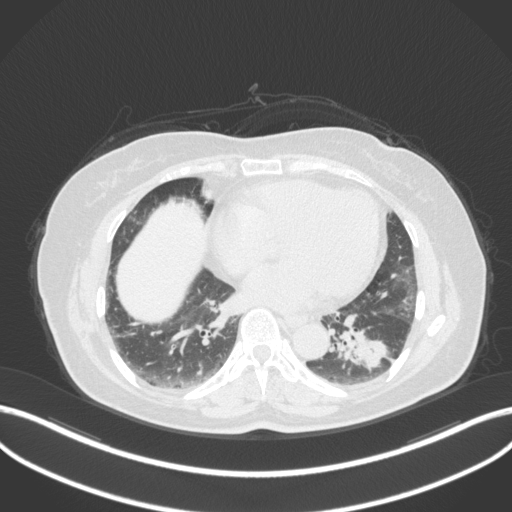
Chest CT, one axial slice; position 145 of 307 along the scan axis; reconstruction kernel B31f; 120 kVp; lung window (W 1500 / L -600 HU); 1 mm slice thickness; 512 × 512 image matrix, field of view 400 × 400 mm. Female patient, age 59 years. From the clinical record (not read from this slice): clinical TNM (as recorded): T2a N0 M0; histopathological grade: G2-3.
Outlined on this slice (rectangle marked by the reading radiologist):
- lung tumour (recorded histology: adenocarcinoma): box from (x=333, y=314) to (x=391, y=373) px